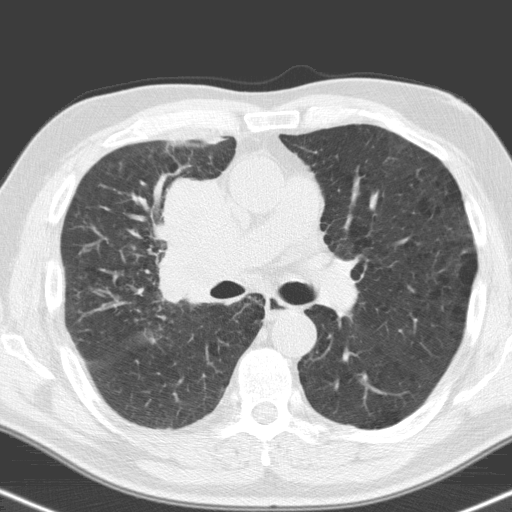
Low-dose screening chest CT, one axial slice; slice 97 of 160 in the series (ordered by position); 120 kVp; lung window (W 1500 / L -600 HU); 3.2 mm slice thickness; 512 × 512 image matrix.
Outlined on this slice (outlined manually by an expert reader):
- lesion 1 (tumor, hilum of right lung): box from (x=162, y=177) to (x=249, y=303) px